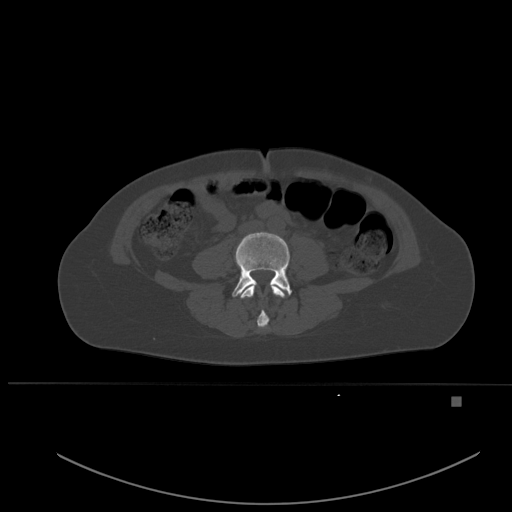
CT including the spine, one axial slice. Bone window (W 1800 / L 400 HU). 1.5 mm slice thickness. 512 × 512 image matrix, field of view 443 × 443 mm. Patient: female, 49 years. Case-level facts recorded for this patient, not image findings: primary cancer: breast.
Outlined on this slice (semi-automatically segmented with operator editing):
- L3 vertebra: box from (x=240, y=284) to (x=285, y=328) px
- L4 vertebra: (x=232, y=232)–(x=292, y=297)